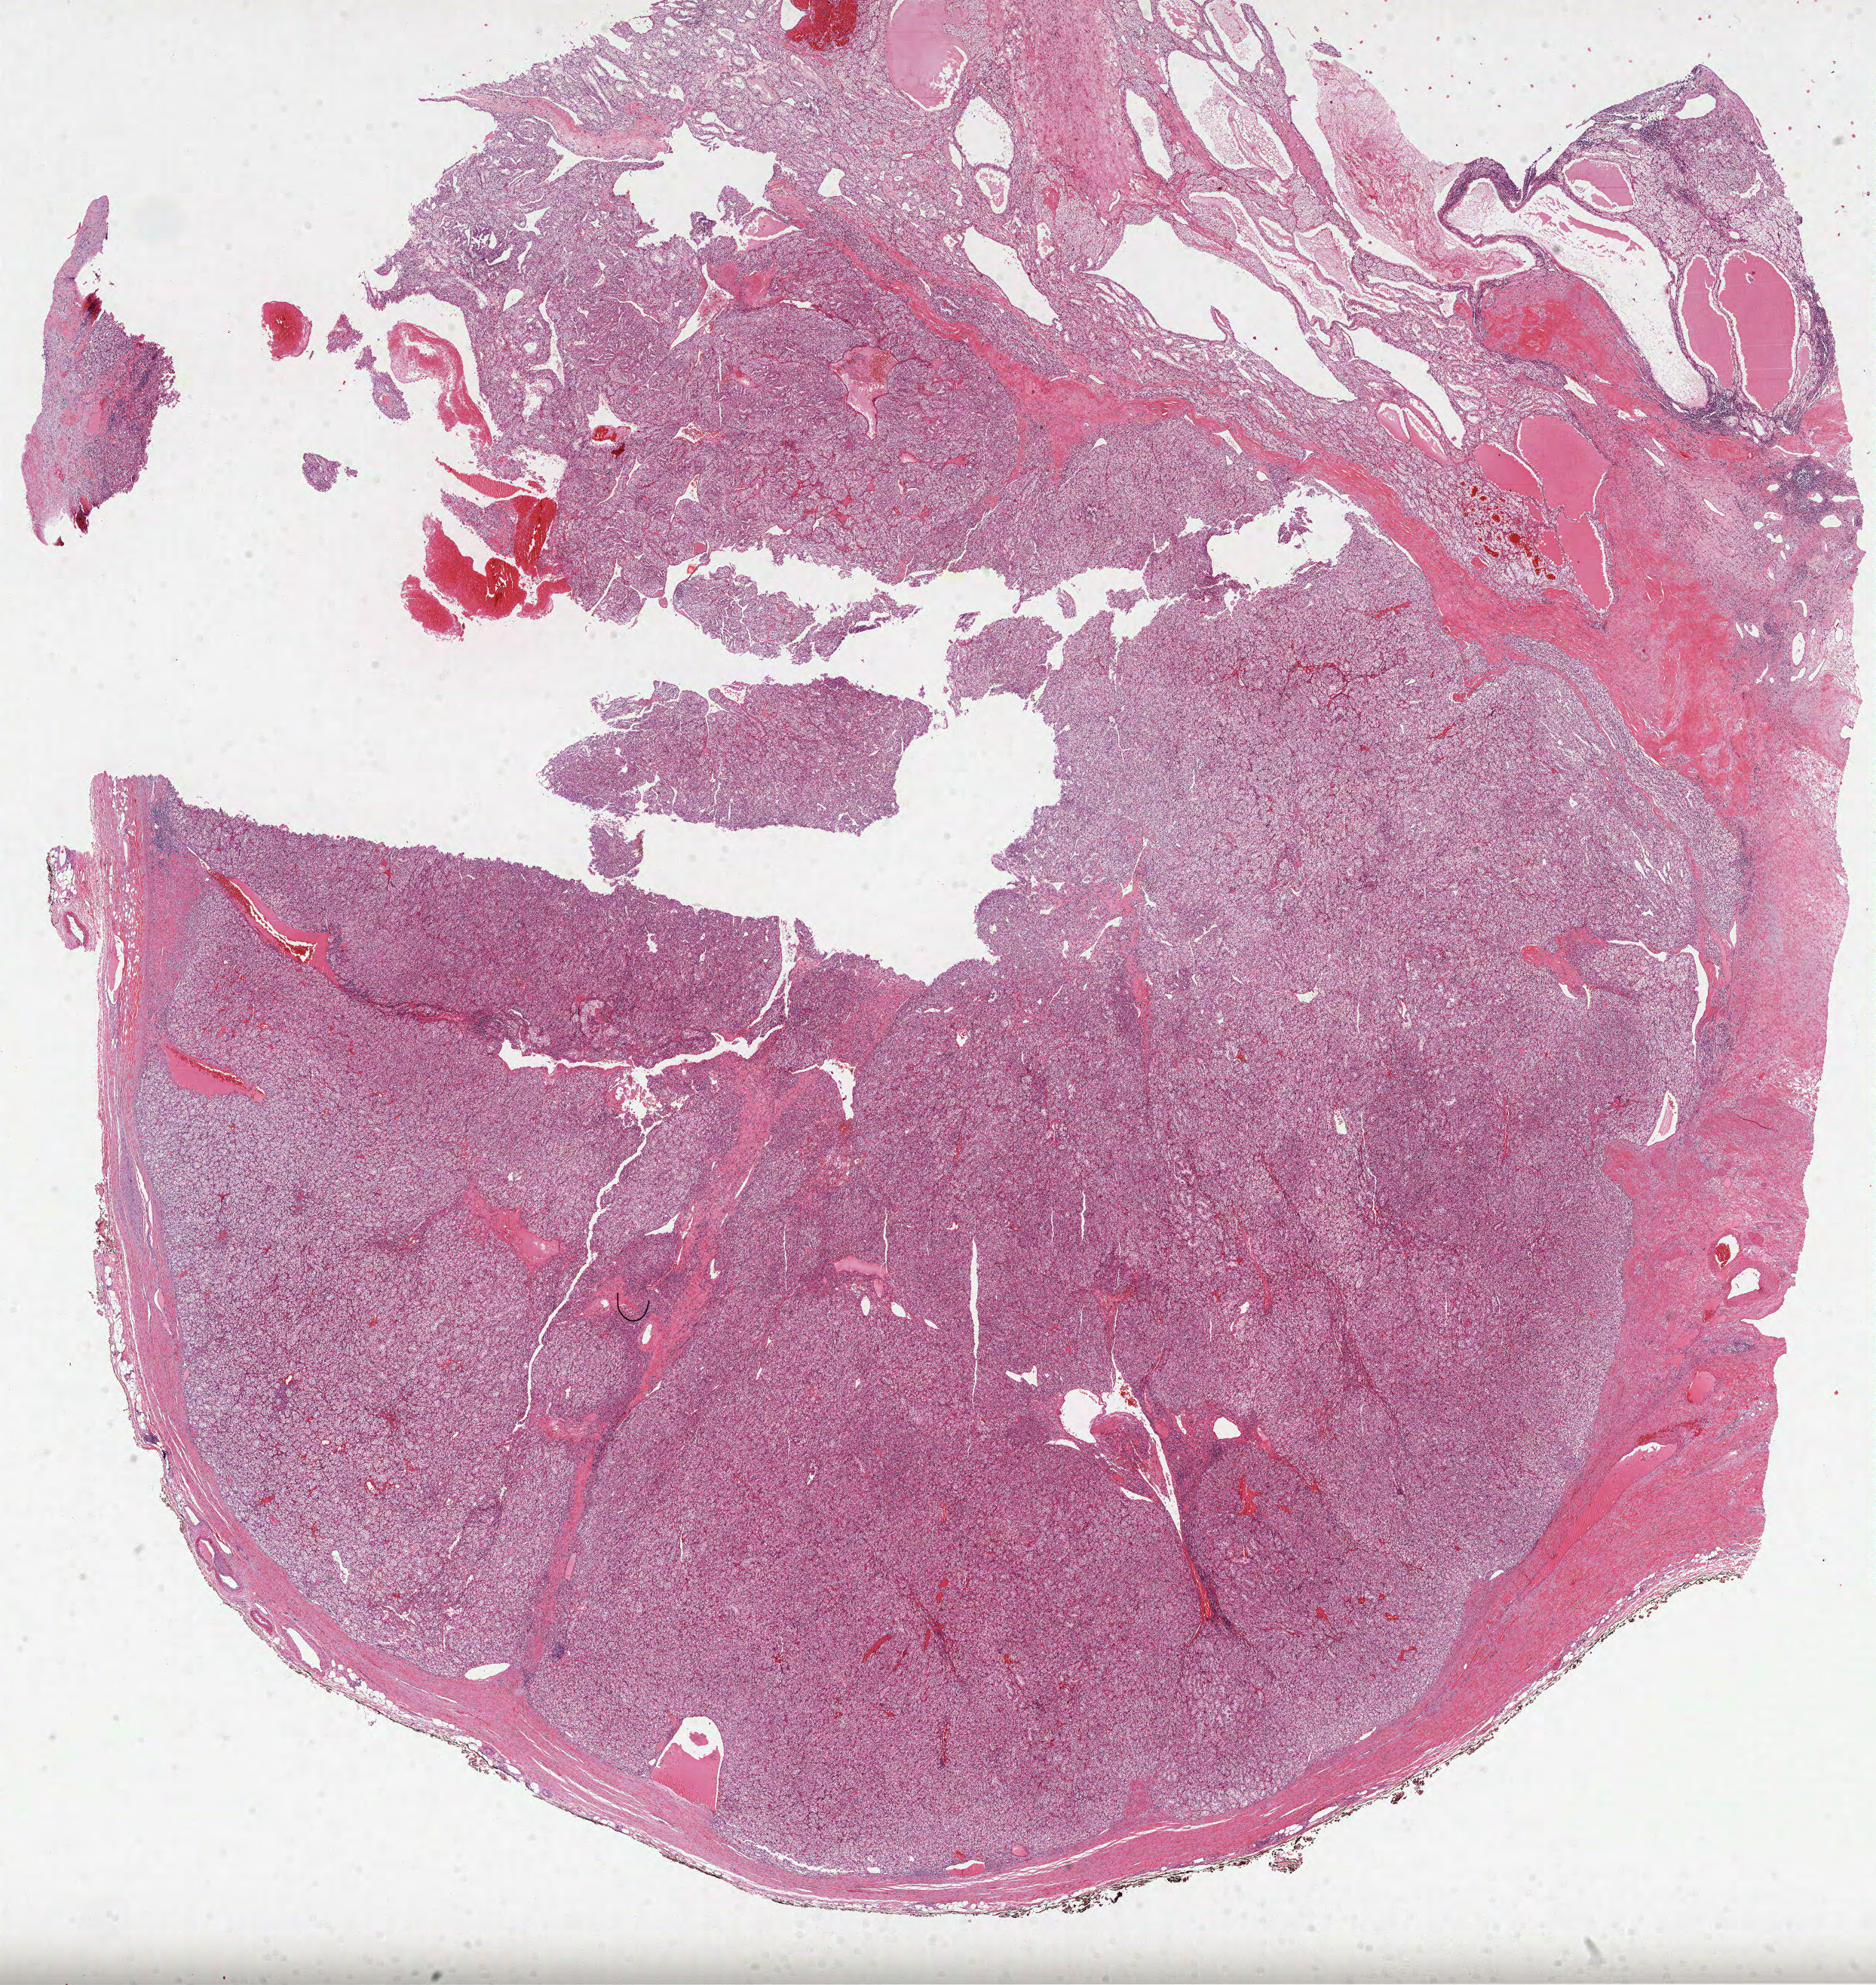
Whole-slide histology image, H&E — low-resolution overview of the scanned area, about 20.1 x 21.2 mm; formalin-fixed paraffin-embedded (FFPE) diagnostic section; primary tumour sample from the kidney. Male, age 45 years at initial diagnosis. Histologic grade: G2 (moderately differentiated).
Diagnosis: Clear cell adenocarcinoma, NOS. Laterality: left. AJCC pathologic stage: II.